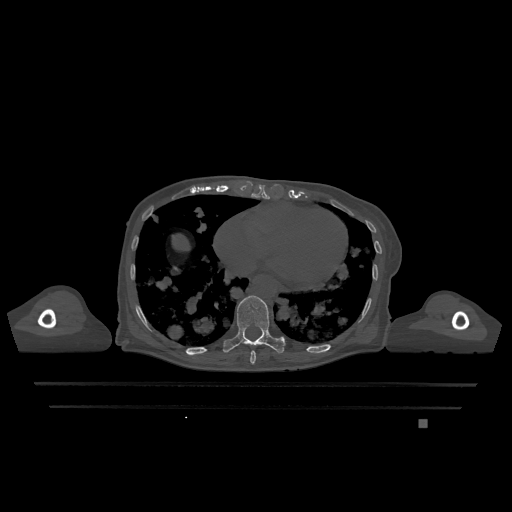
CT including the spine, one axial slice; position 651 of 1317 along the scan axis; bone window (W 1800 / L 400 HU); 512 × 512 image matrix. Female patient, age 74 years. From the clinical record (not read from this slice): primary cancer: lung; vertebrae with lytic lesions (as recorded): T1, T4, T5, T6, L4, L5.
Outlined on this slice (semi-automatically segmented with operator editing):
- T10 vertebra: bounding box (x1, y1, x2, y2) in pixels: (223, 295, 285, 353)
- T9 vertebra: (250, 351, 256, 364)